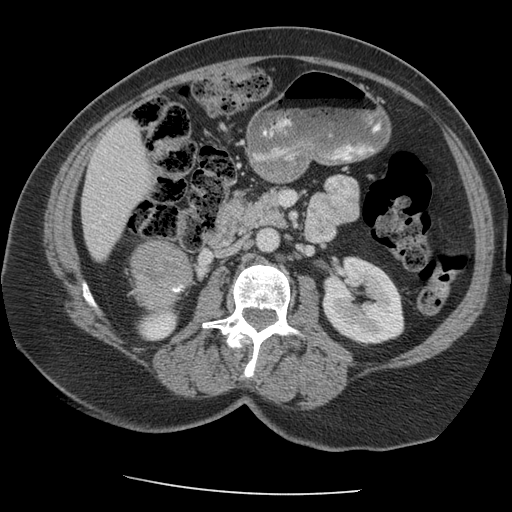
Contrast-enhanced abdominal CT, one axial slice; slice 106 of 163 in the series (ordered by position); reconstruction kernel STANDARD; intravenous contrast given; soft-tissue window (W 400 / L 40 HU); 512 × 512 image matrix. Patient: female, 70 years. Case-level facts recorded for this patient, not image findings: diagnosis: adrenocortical carcinoma; tumour side: right adrenal; tumour size at pathology: 9.5 cm; Ki-67 index: 5 %.
Structures marked on this image (semi-automatic segmentation, software-assisted and operator-edited):
- mass: bounding box (x1, y1, x2, y2) in pixels: (132, 241, 191, 310)